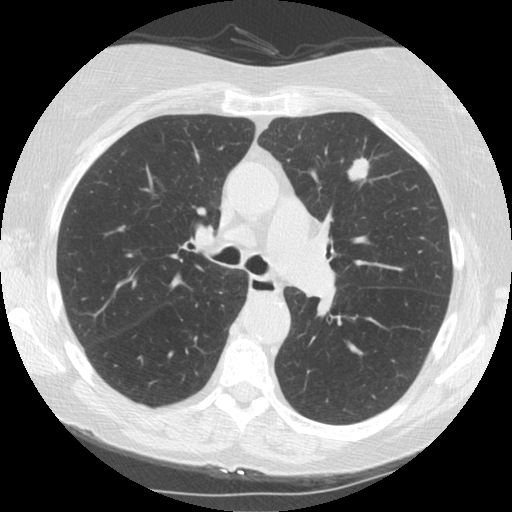
Low-dose screening chest CT, one axial slice; position 93 of 153 along the scan axis; reconstruction kernel STANDARD; 120 kVp; lung window (W 1500 / L -600 HU); 2.5 mm slice thickness; 512 × 512 image matrix, field of view 330 × 330 mm.
Structures marked on this image (manually delineated by an expert):
- lesion 1 (tumor, upper lobe of left lung): bounding box [x1, y1, x2, y2] px = [348, 158, 369, 180]